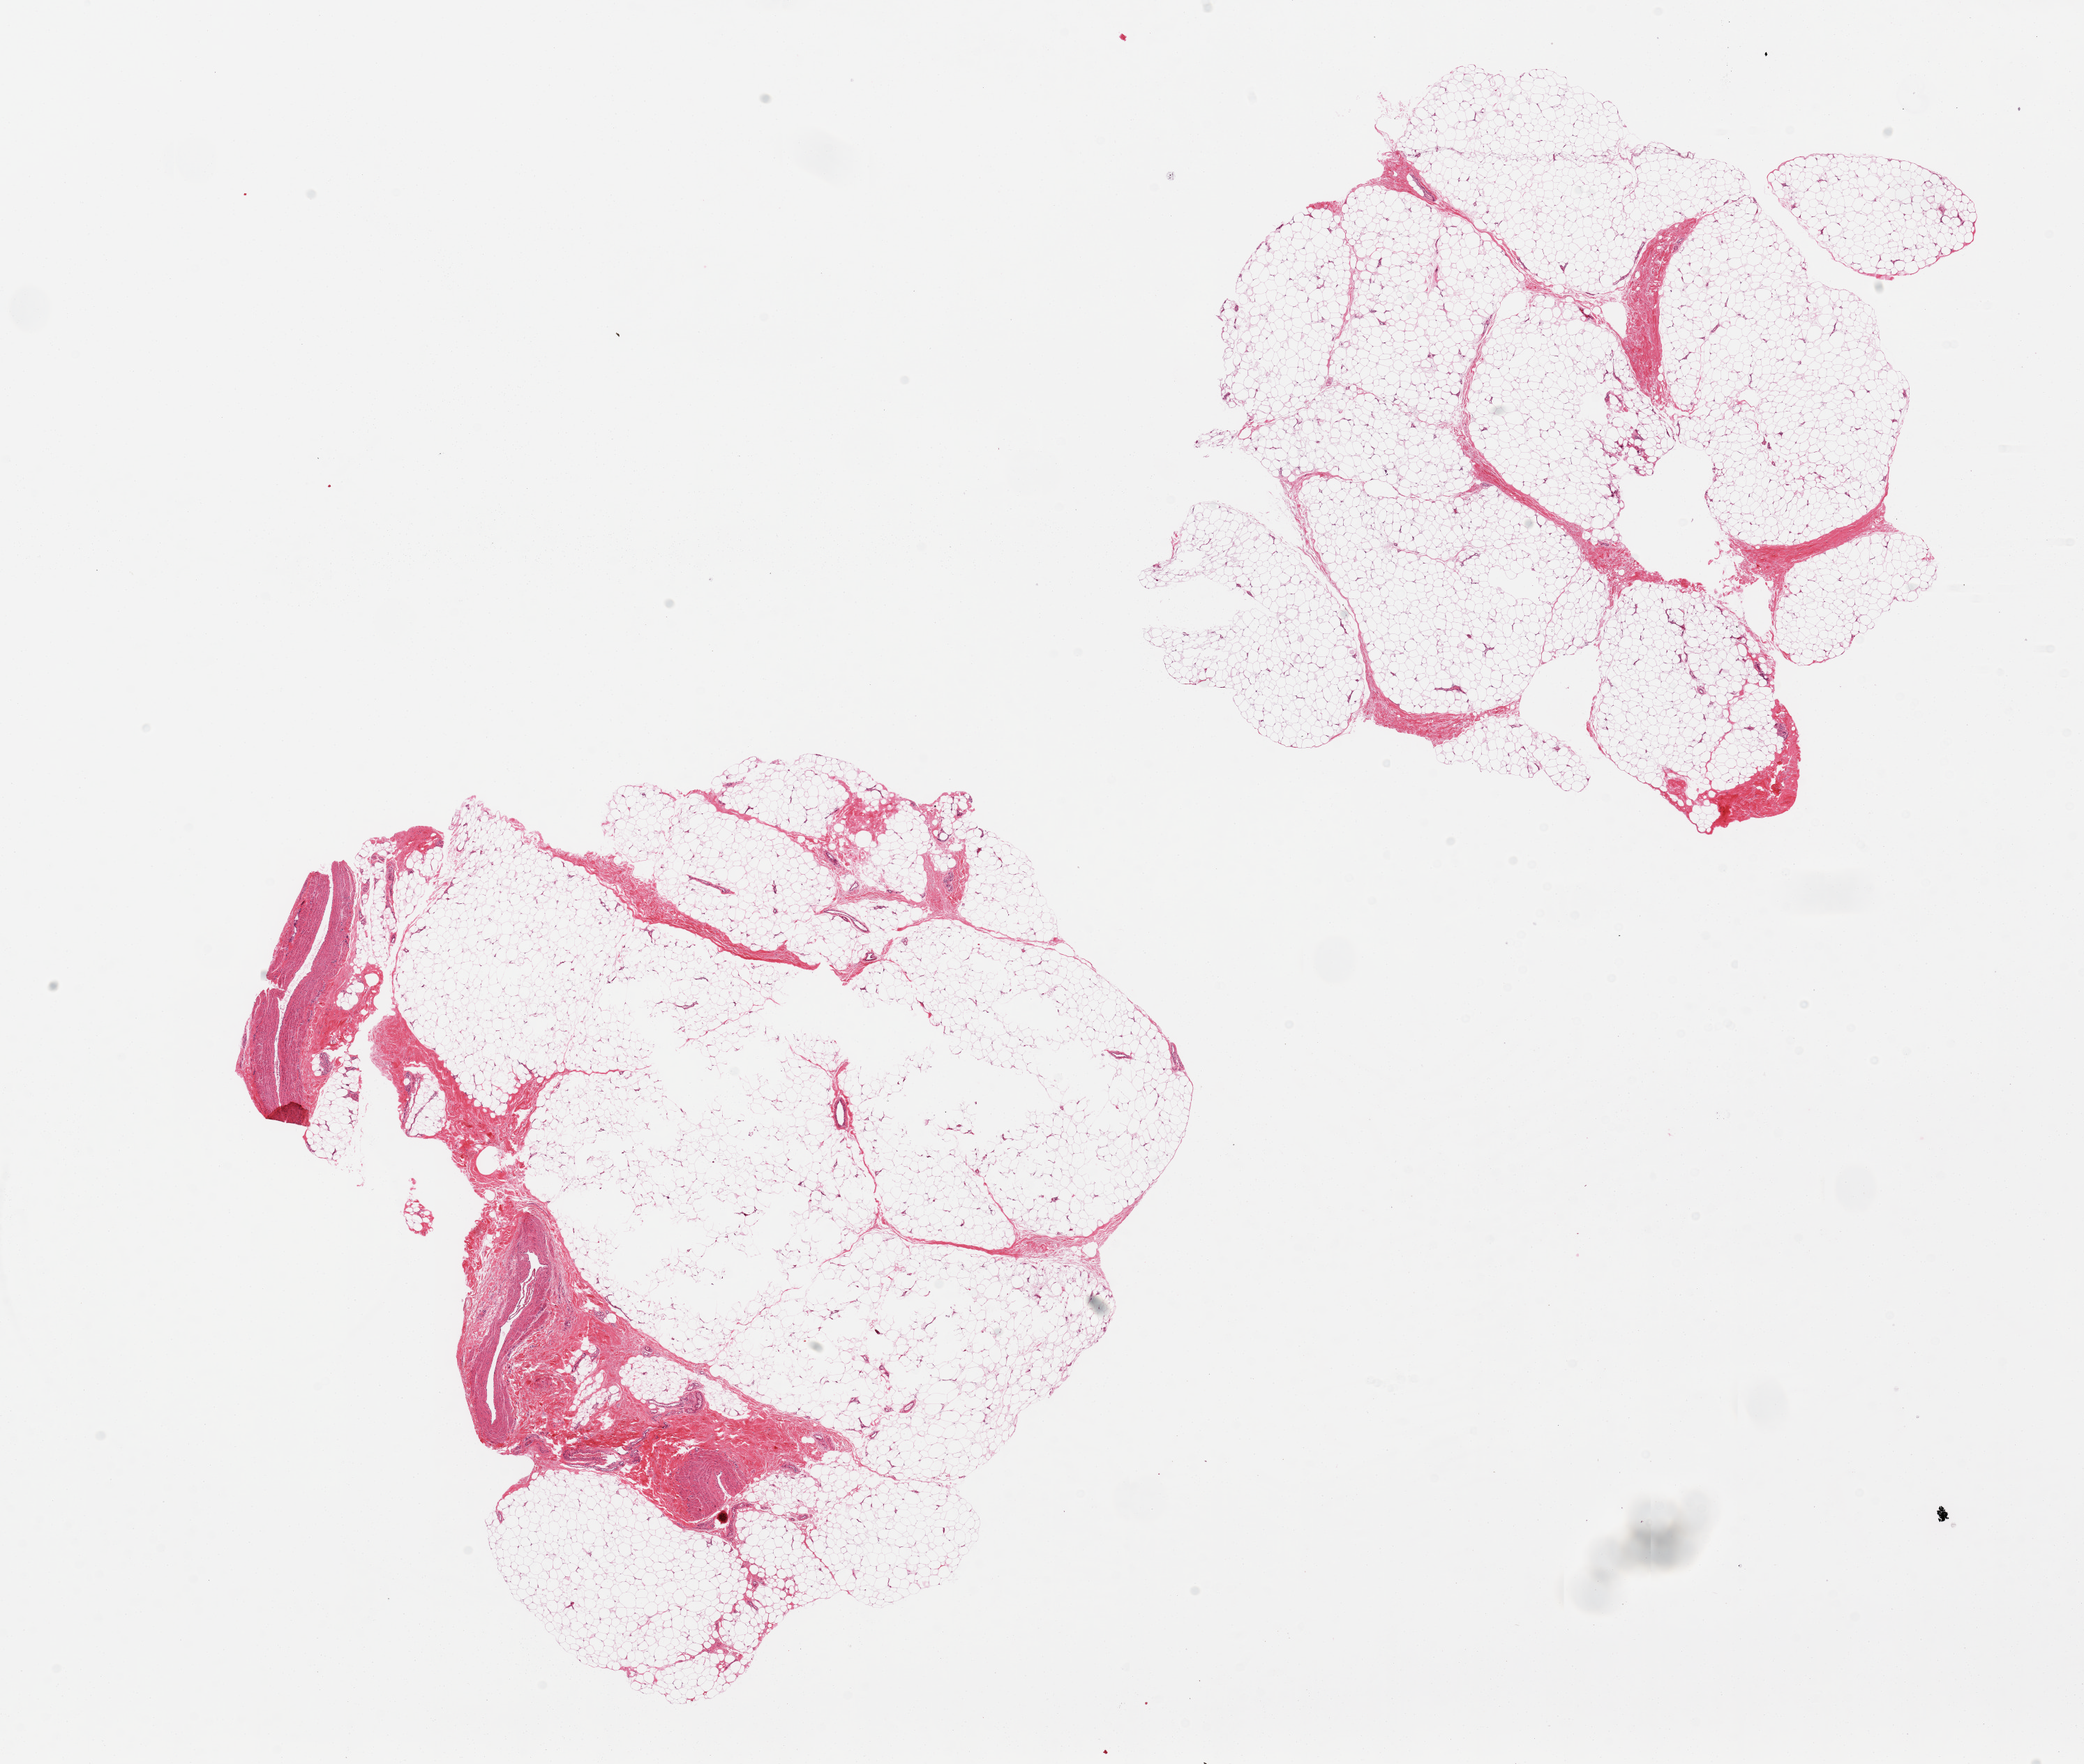
H&E whole-slide image, brightfield — low-resolution overview of the scanned area, about 23.6 x 20.0 mm; PAXgene-fixed, paraffin-embedded tissue; sampled site (target tissue): adipose tissue; tissue donor sample. Donor sex: male.
Review note (as recorded): 2 pieces, one includes several large vessels.